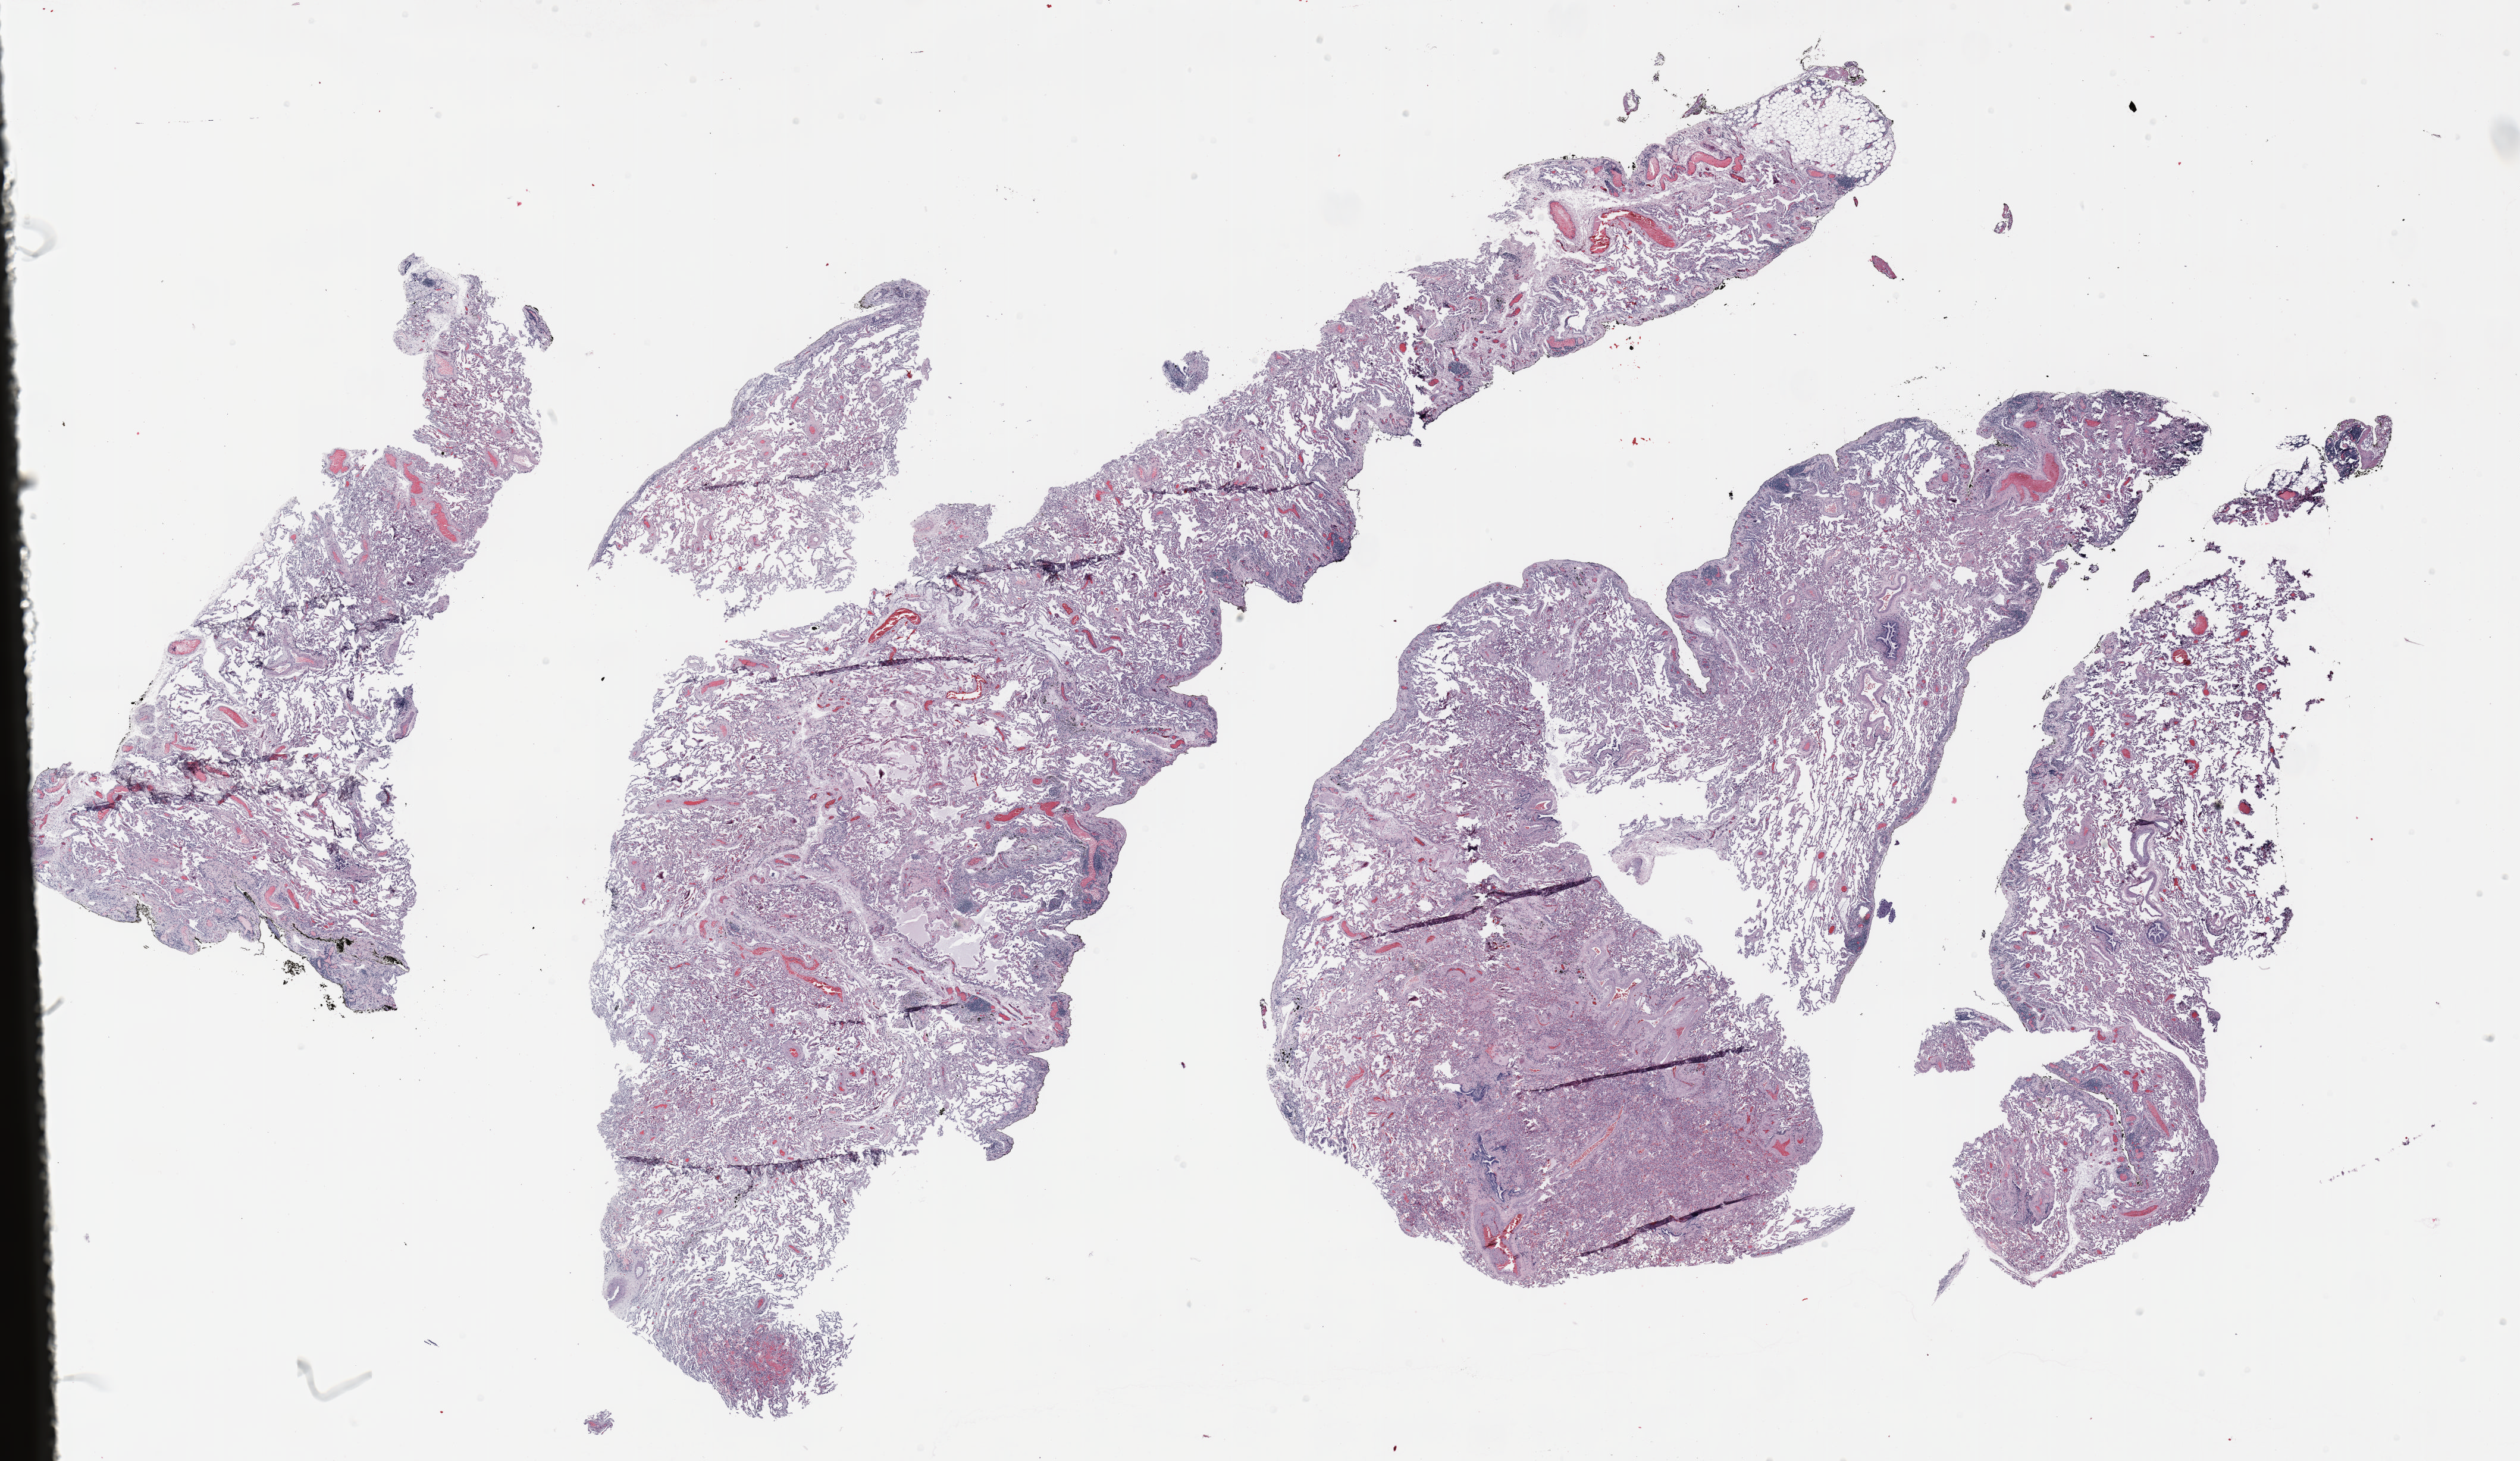
Whole-slide histology image, Hematoxylin and eosin (H&E) stained, low-resolution overview of the scanned area, about 34.0 x 19.7 mm, FFPE section, lung tissue. Male, age 68 at enrolment. Grade: poorly differentiated (G3).
- stage (AJCC 6th edition): IV
- primary tumour location (clinical record): left upper lobe
- participant's lung-cancer diagnosis: Non-small cell carcinoma (ICD-O-3 8046/3)
- tumour size (pathology): 30 mm